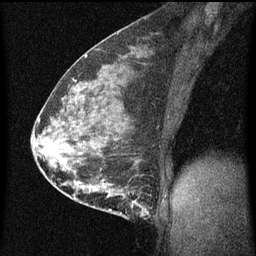
Breast MRI (dynamic contrast-enhanced), one sagittal slice; position 31 of 60 along the scan axis; dynamic contrast-enhanced series, image 2 of 3 at this slice position (ordered by acquisition); 1.5 T; TE 4.2 ms, TR 8 ms; 2 mm slice thickness; 256 × 256 image matrix, field of view 180 × 180 mm. Patient: female, 35 years.
Structures marked on this image (semi-automatically segmented with operator editing):
- analysis volume of interest (the breast-tissue region the enhancement analysis was run in; not a lesion): bounding box [x1, y1, x2, y2] px = [110, 178, 155, 219]
- tumour enhancement mask (voxels above the 70 % enhancement threshold inside the analysis volume of interest): [110, 192, 150, 217]